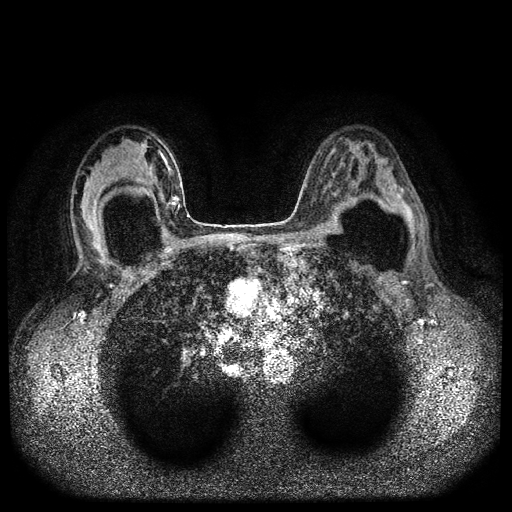
Breast MRI (dynamic contrast-enhanced, multi-phase), one axial slice; slice 60 of 116 in the series (ordered by position); dynamic contrast-enhanced series, time point 2 of 5 at this slice position (early post-contrast); 1.5 T; TE 2.6 ms, TR 5.4 ms; 512 × 512 image matrix, field of view 340 × 340 mm. Female patient, age 42 years.
Outlined on this slice (semi-automatic segmentation, software-assisted and operator-edited):
- breast lesion (labelled 'tumour' in the annotation; benign lesions carry a separate 'benign' label): bounding box (x1, y1, x2, y2) in pixels: (168, 196, 180, 209)